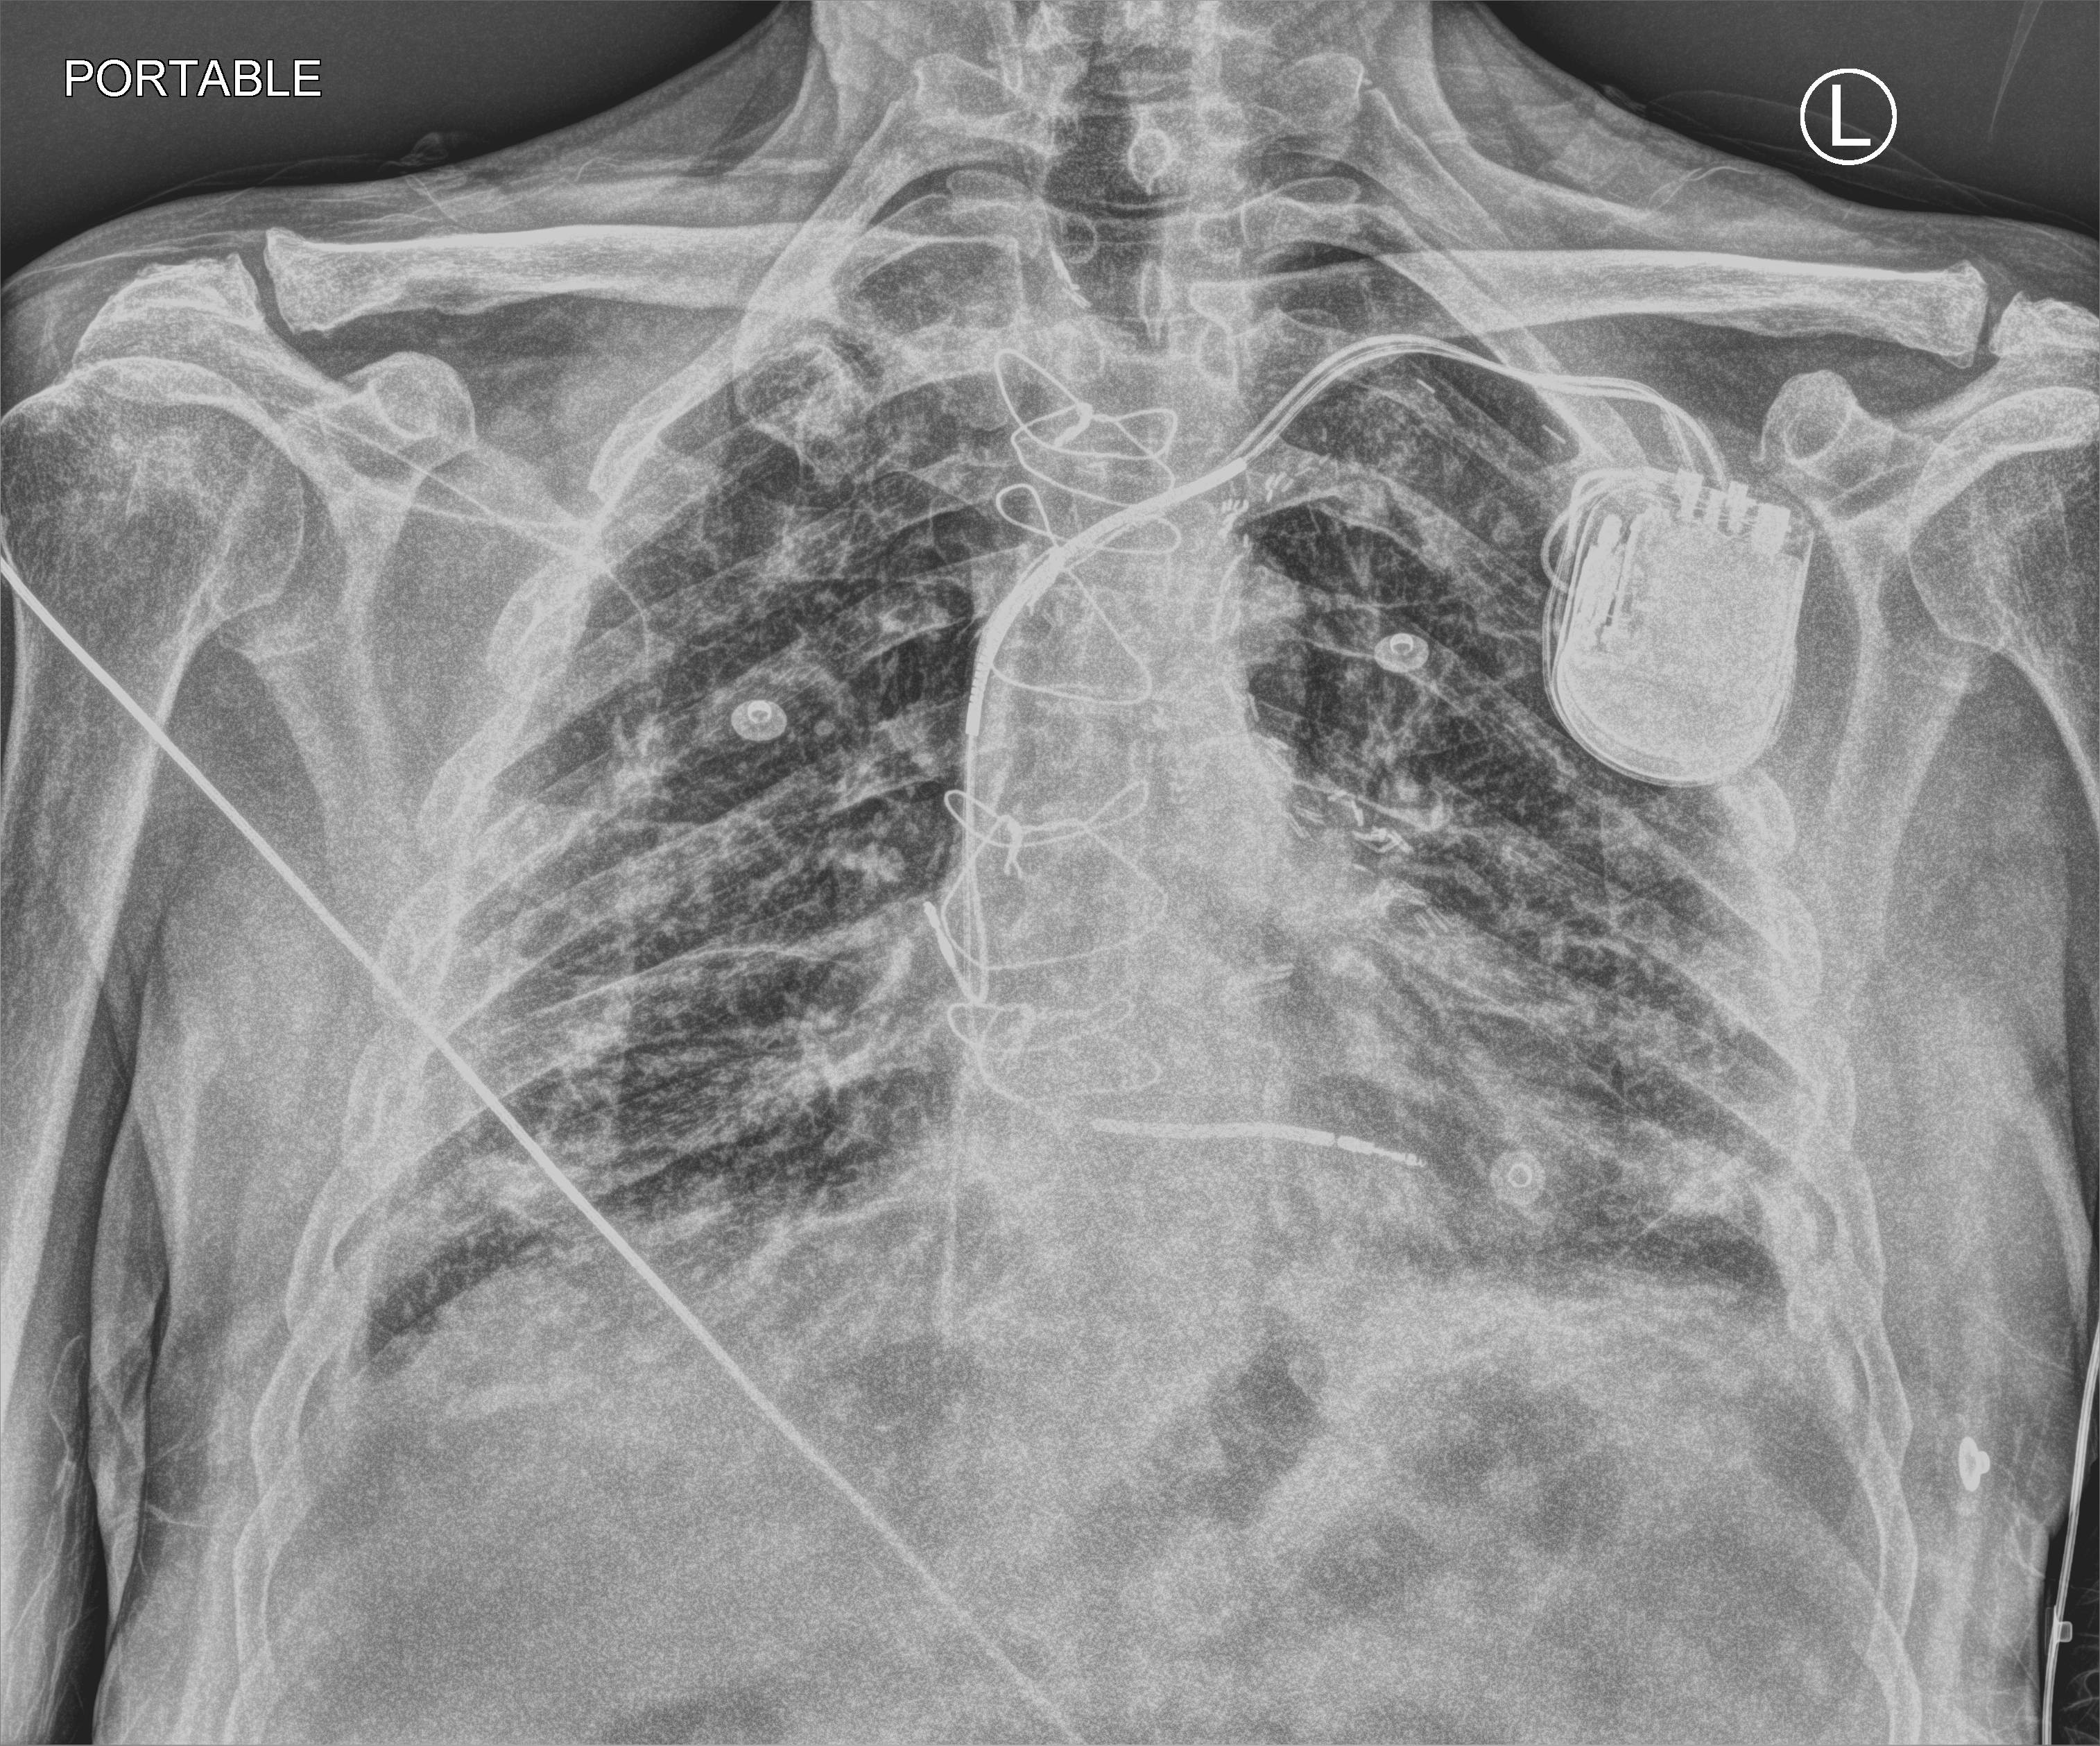
Chest X-ray (portable). Patient hospitalised with COVID-19; male, aged 75–90 years.
From the hospital-stay record, not from the radiograph (when in the stay this image was taken is not recorded): mechanically ventilated during this hospital stay: no.